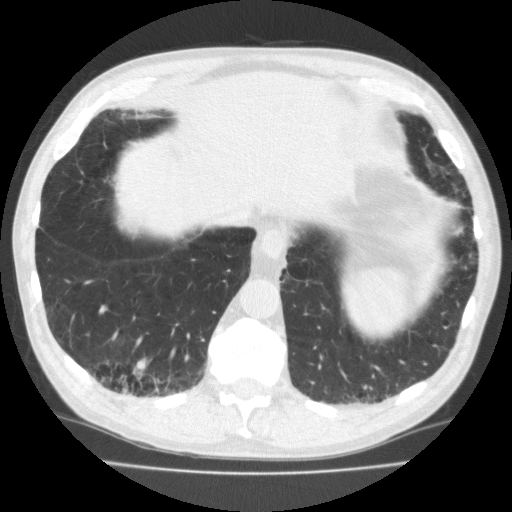
Chest CT (low-dose screening protocol), one axial image; second annual screen; lung window (W 1500 / L -600 HU); 2 mm slice thickness; 120 kVp. Male, age 70 years at enrolment.
Expert-annotated lung lesion, bounding box <98,342,161,397> (left, top, right, bottom; pixels). Reader record for this screening exam (exam-level; its link to the box is not recorded): non-calcified nodule or mass ≥4 mm, right lower lobe, 18 × 13 mm, spiculated (stellate) margins, soft tissue attenuation, pre-existing on the prior screen: no. Lung cancer was diagnosed 64 days after this screen: squamous cell carcinoma, NOS, right lower lobe, moderately differentiated (G2), stage IA (AJCC 6th edition), 20 mm at pathology.